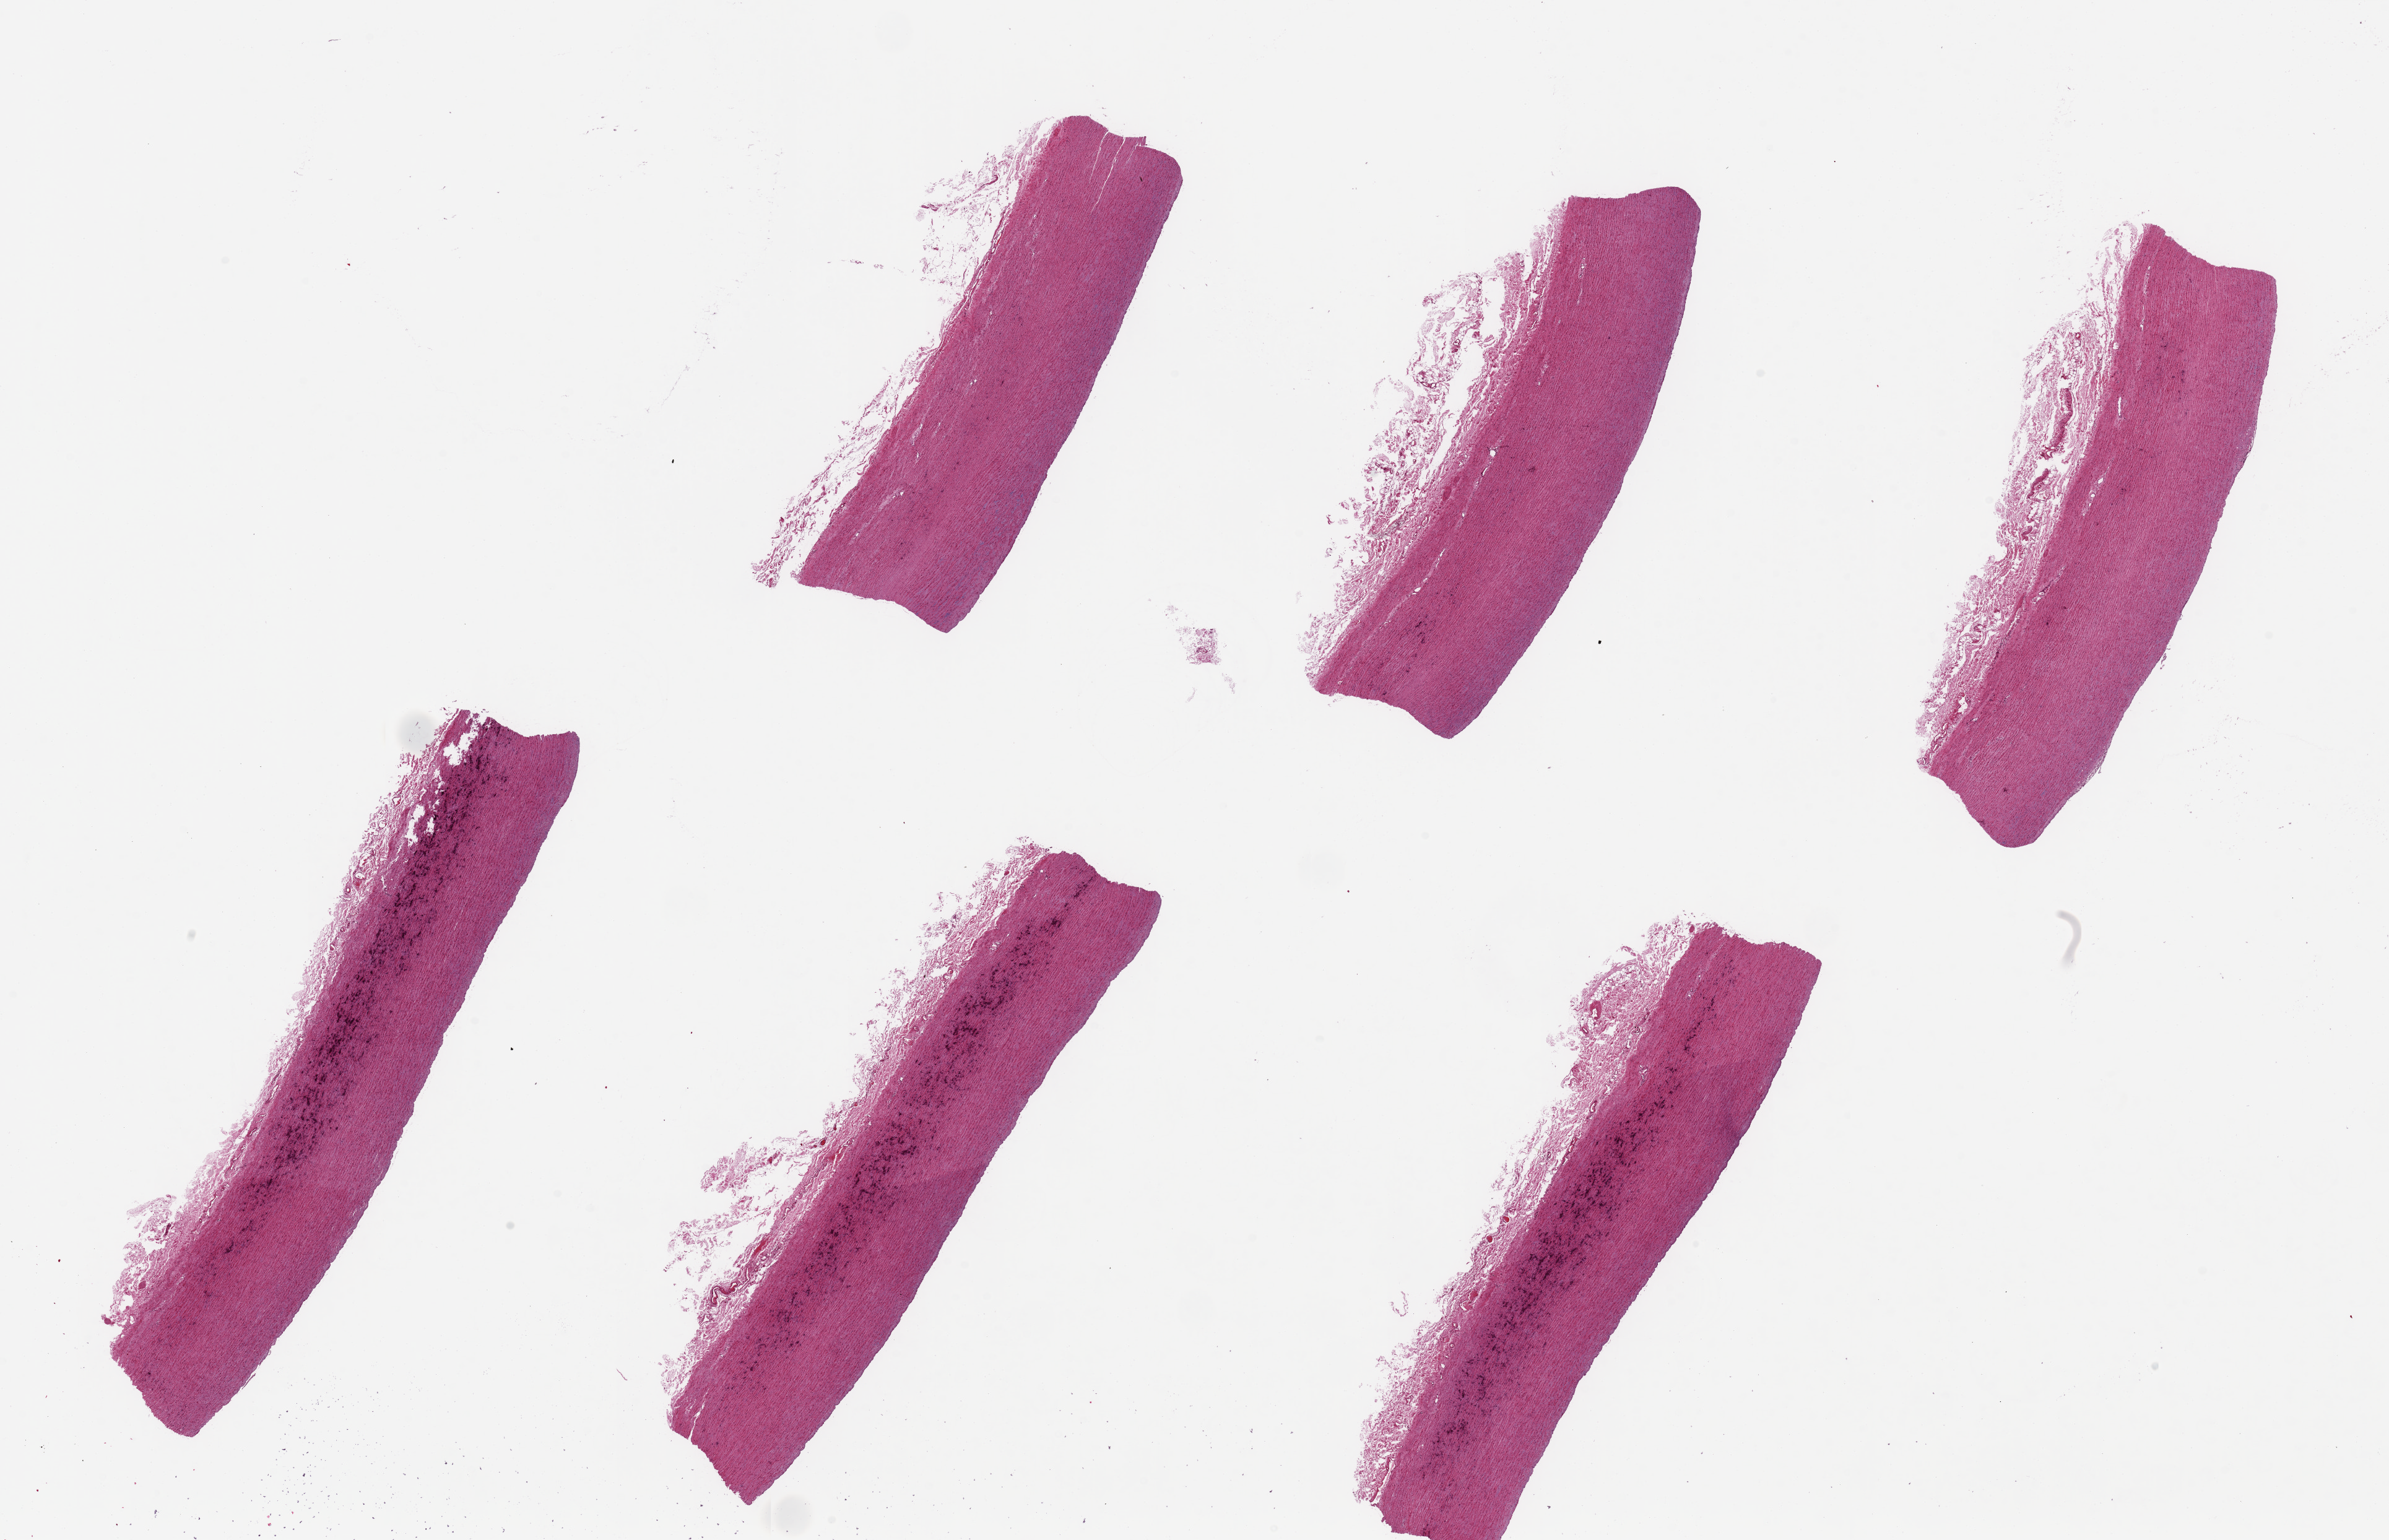
Hematoxylin and eosin (H&E) whole-slide image, low-resolution overview of the scanned area, about 30.5 x 19.7 mm. PAXgene-fixed paraffin-embedded (PFPE) section. Sampled site (target tissue): aorta. Tissue donor sample.
Reviewer comment on this tissue sample: 6 pieces up to 10x2 mm; mild linear medial calcification; minimal adipose.